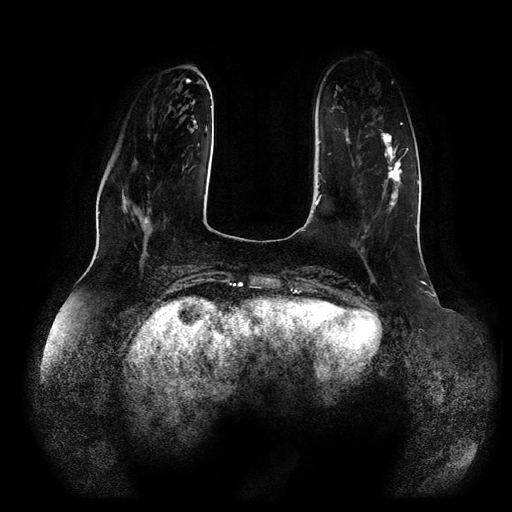
Breast MRI (dynamic contrast-enhanced, multi-phase), one axial slice. Slice 28 of 116 in the series (ordered by position). Dynamic contrast-enhanced series, time point 2 of 5 at this slice position (early post-contrast). 1.5 T. TE 2.5 ms, TR 5.2 ms. 2 mm slice thickness. 512 × 512 image matrix, field of view 400 × 400 mm. Patient: female, 66 years.
Outlined on this slice (semi-automatic segmentation, software-assisted and operator-edited):
- breast lesion (labelled 'tumour' in the annotation; benign lesions carry a separate 'benign' label): bounding box <380,130,409,218> (left, top, right, bottom; pixels)